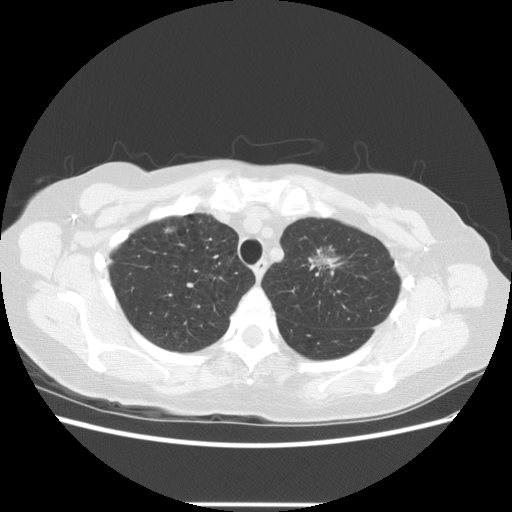
Chest CT (low-dose screening protocol), one axial image; third annual screen; lung window (W 1500 / L -600 HU); standard (soft-tissue) reconstruction kernel (STANDARD); 140 kVp; slice 101 of 126 in the series; 512 × 512 image matrix, field of view 360 × 360 mm. Female, age 65 years at enrolment. Former smoker at enrolment.
Expert-annotated lung lesion, bounding box <291,227,368,294> (left, top, right, bottom; pixels). Screening reader's record for this exam (one nodule recorded; not confirmed to be the boxed lesion): non-calcified nodule or mass ≥4 mm, left upper lobe, 17 × 14 mm, poorly defined margins, ground glass attenuation, pre-existing on the prior screen: yes; interval growth: yes. Official screen result: positive, other. Lung cancer was diagnosed 96 days after this screen: adenocarcinoma, NOS, left upper lobe, moderately differentiated (G2), stage IA (AJCC 6th edition), 30 mm at pathology.